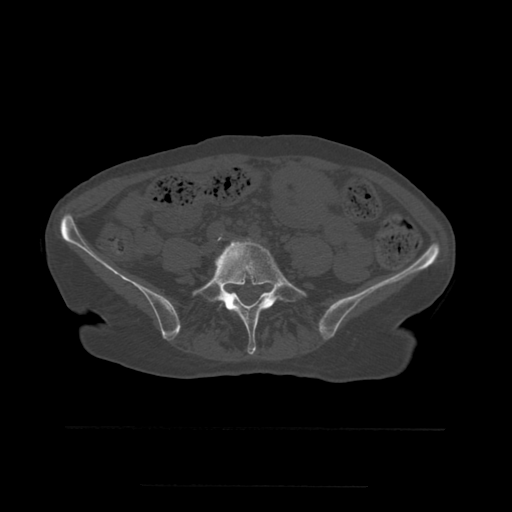
CT including the spine, one axial slice; bone window (W 1800 / L 400 HU); 1.25 mm slice thickness; 512 × 512 image matrix, field of view 350 × 350 mm. Patient age 58 years. Case-level facts recorded for this patient, not image findings: primary cancer: lung.
Outlined on this slice (semi-automatic segmentation, software-assisted and operator-edited):
- L5 vertebra: box from (x=193, y=239) to (x=302, y=355) px